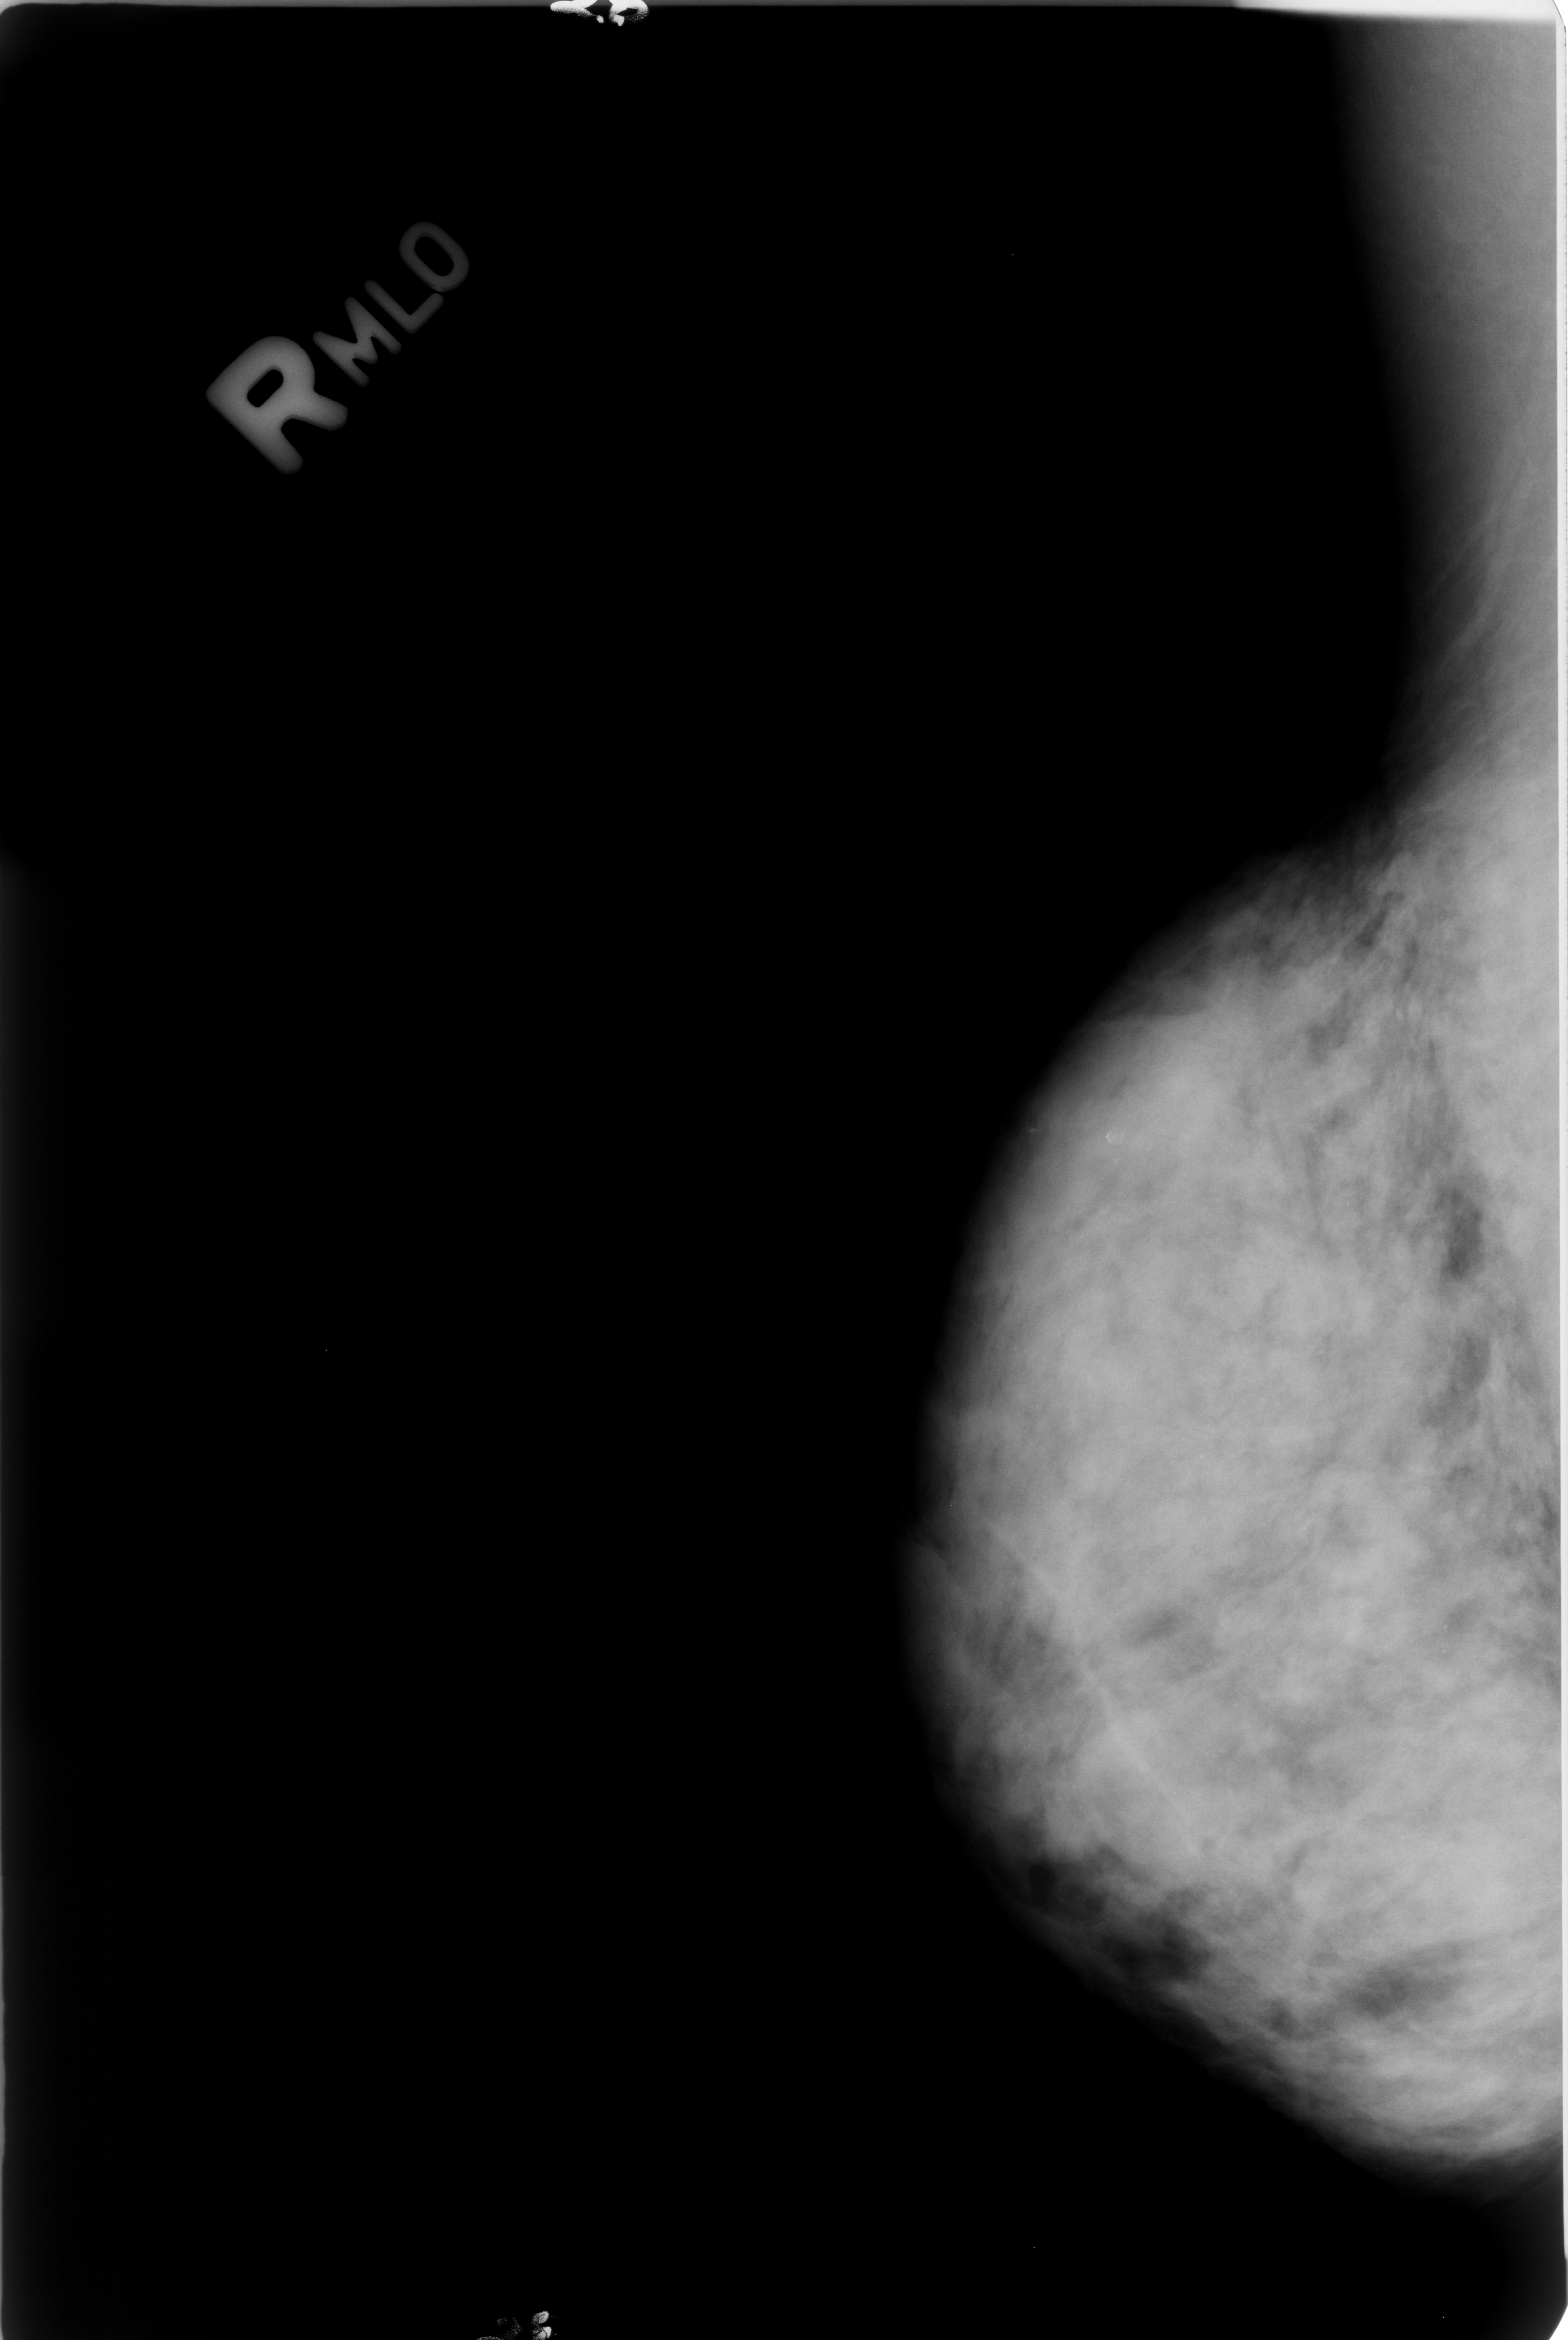
Mammogram (digitized film); right breast; MLO view; breast composition: extremely dense (BI-RADS density category 4 of 4).
Calcifications, morphology lucent center; BI-RADS assessment category 2; subtlety rating 3 on a 1 (subtle) to 5 (obvious) scale; benign; no additional work-up was recommended (benign without callback).